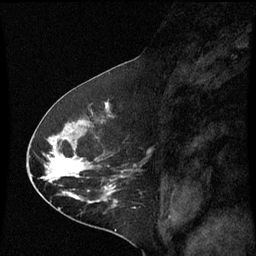
Breast MRI (dynamic contrast-enhanced), one sagittal slice; position 33 of 60 along the scan axis; dynamic contrast-enhanced series, image 2 of 3 at this slice position (ordered by acquisition); 1.5 T; TE 4.2 ms, TR 8.9 ms; 2 mm slice thickness; 256 × 256 image matrix. Patient: female, 53 years. Case-level facts recorded for this patient, not image findings: setting: breast cancer imaged before/during neoadjuvant chemotherapy; receptor status: HR-positive, HER2-negative.
Outlined on this slice (semi-automatically segmented with operator editing):
- analysis volume of interest (the breast-tissue region the enhancement analysis was run in; not a lesion): box from (x=32, y=100) to (x=137, y=221) px
- tumour enhancement mask (voxels above the 70 % enhancement threshold inside the analysis volume of interest): (x=46, y=104)–(x=111, y=195)